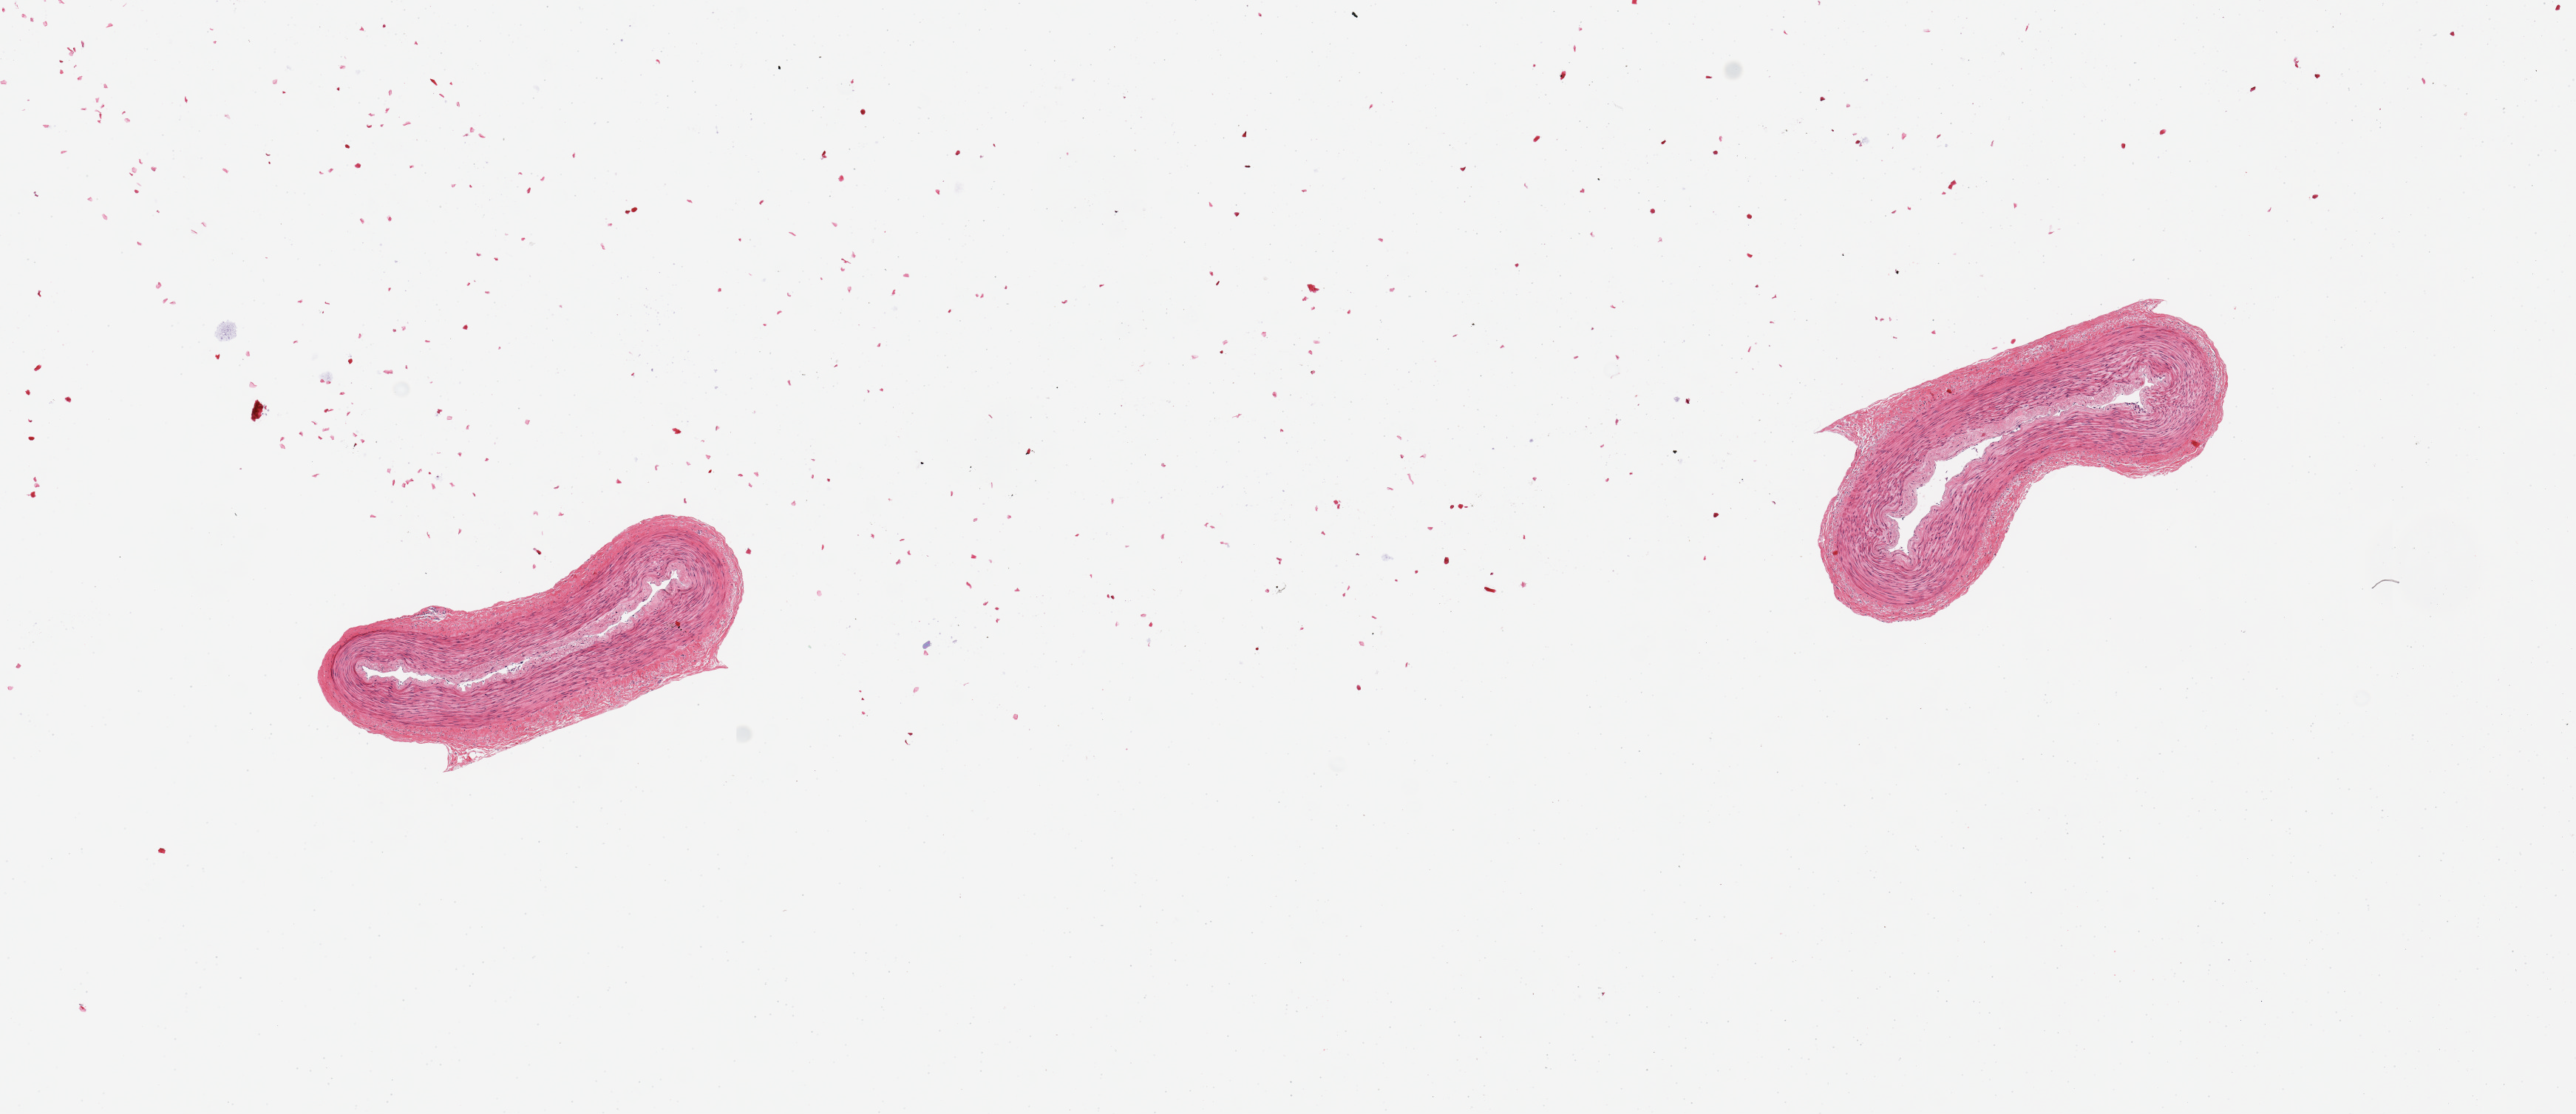
Whole-slide image, haematoxylin and eosin stain — shown as a low-resolution overview of the whole scanned area (about 13.8 x 6.0 mm); PAXgene-fixed, paraffin-embedded tissue; sampled site (target tissue): tibial artery; donor tissue sample. Donor sex: female.
* review note (as recorded): 2 pieces, clean, no atherosis